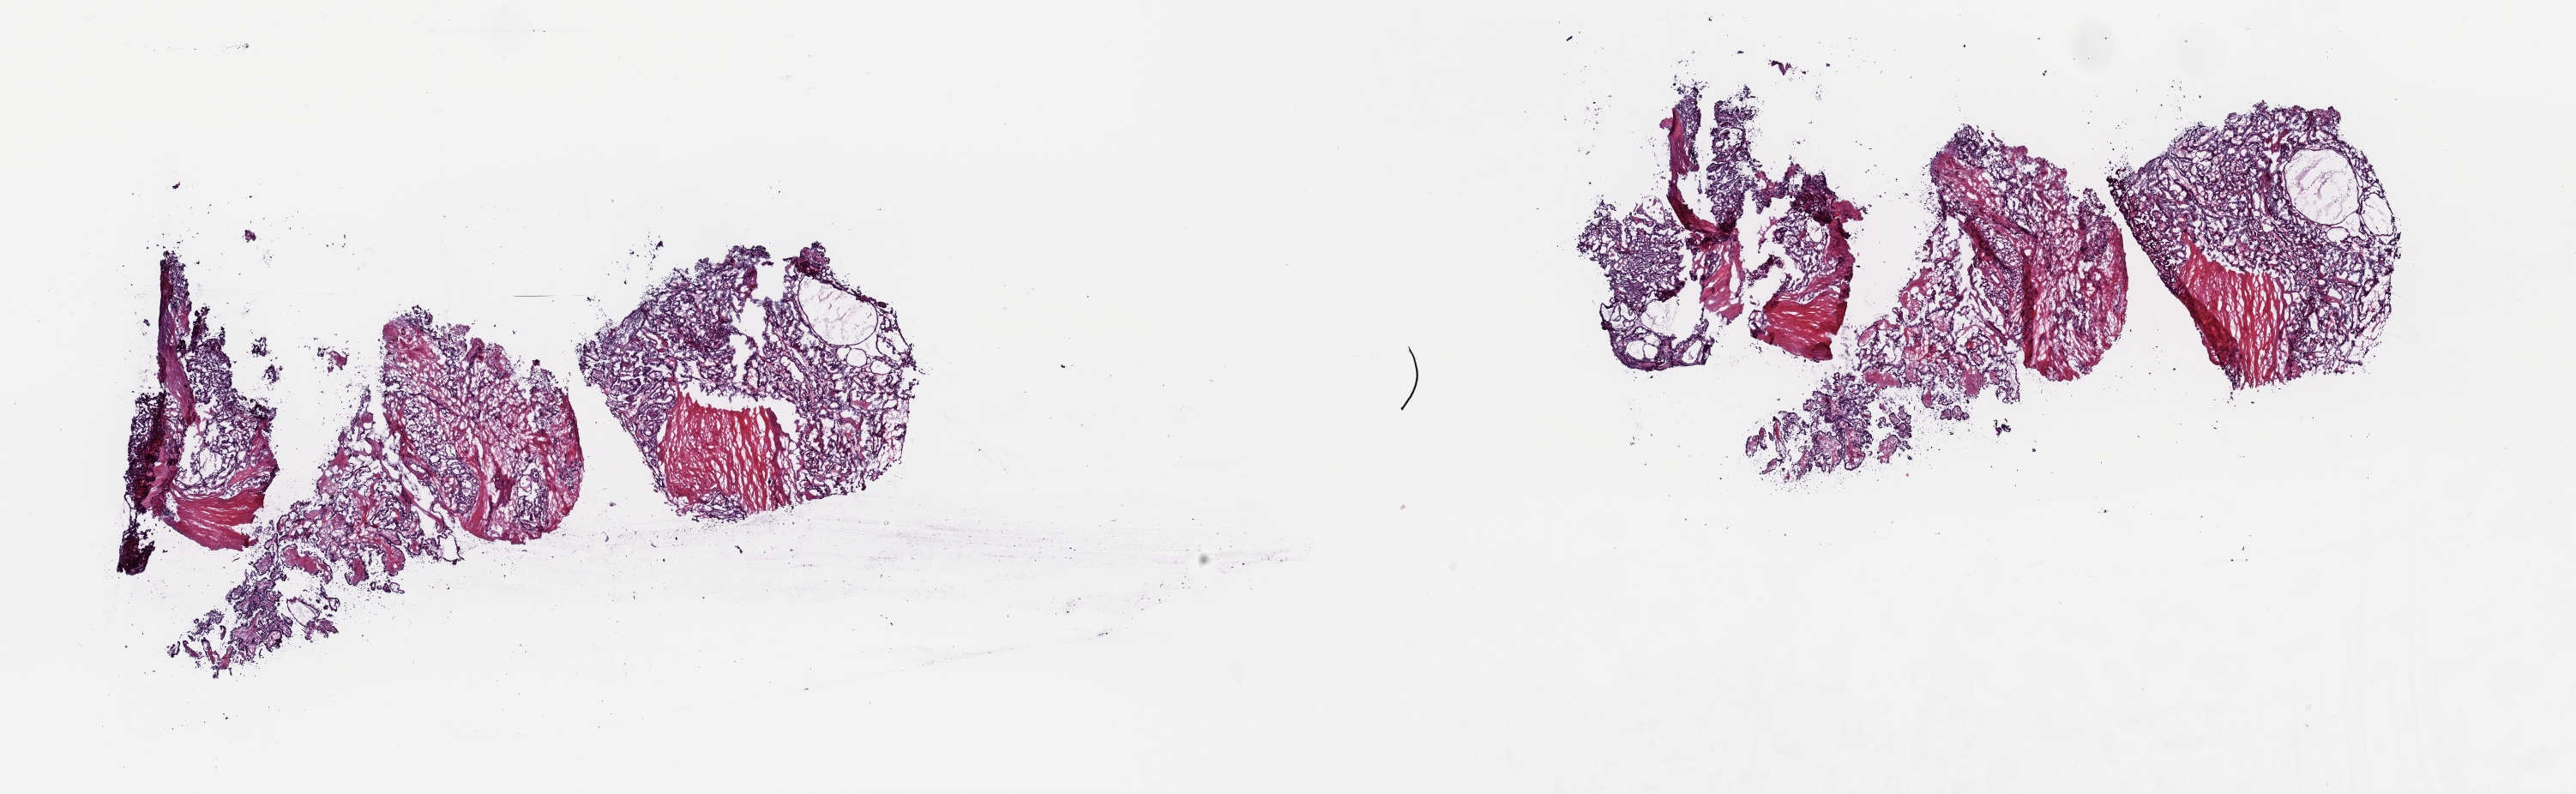
H&E whole-slide image — low-resolution overview of the scanned area, about 23.7 x 7.3 mm. Frozen section from the top of the tissue portion. Primary tumour sample from the thyroid. Patient: female, age at initial diagnosis 35 years. Composition of this section per pathologist review: tumour cells 80%, tumour nuclei 80%, normal cells 0%, stromal cells 20%, necrosis 0%. Infiltration values recorded for this section: lymphocyte infiltration 5%, monocyte infiltration 0%, neutrophil infiltration 0%.
Lymph nodes positive (case pathology): 14 of 44 examined. AJCC pathologic stage: I. Diagnosis: Papillary adenocarcinoma, NOS (thyroid gland). Laterality: left.